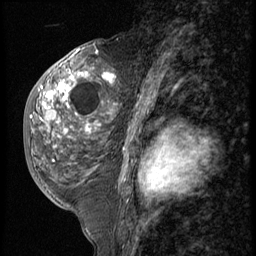
Breast MRI (dynamic contrast-enhanced), one sagittal slice. Slice 31 of 56 in the series (ordered by position). 3 images stored at this slice position (order not interpretable as contrast timing). 1.5 T. TE 4.2 ms, TR 9 ms. 256 × 256 image matrix, field of view 180 × 180 mm. Female patient, age 50 years. From the clinical record (not read from this slice): setting: breast cancer imaged before/during neoadjuvant chemotherapy; receptor status: triple-negative.
Outlined on this slice (semi-automatically segmented with operator editing):
- analysis volume of interest (the breast-tissue region the enhancement analysis was run in; not a lesion): bounding box <25,50,119,191> (left, top, right, bottom; pixels)
- tumour enhancement mask (voxels above the 140 % enhancement threshold inside the analysis volume of interest): <31,73,116,133>